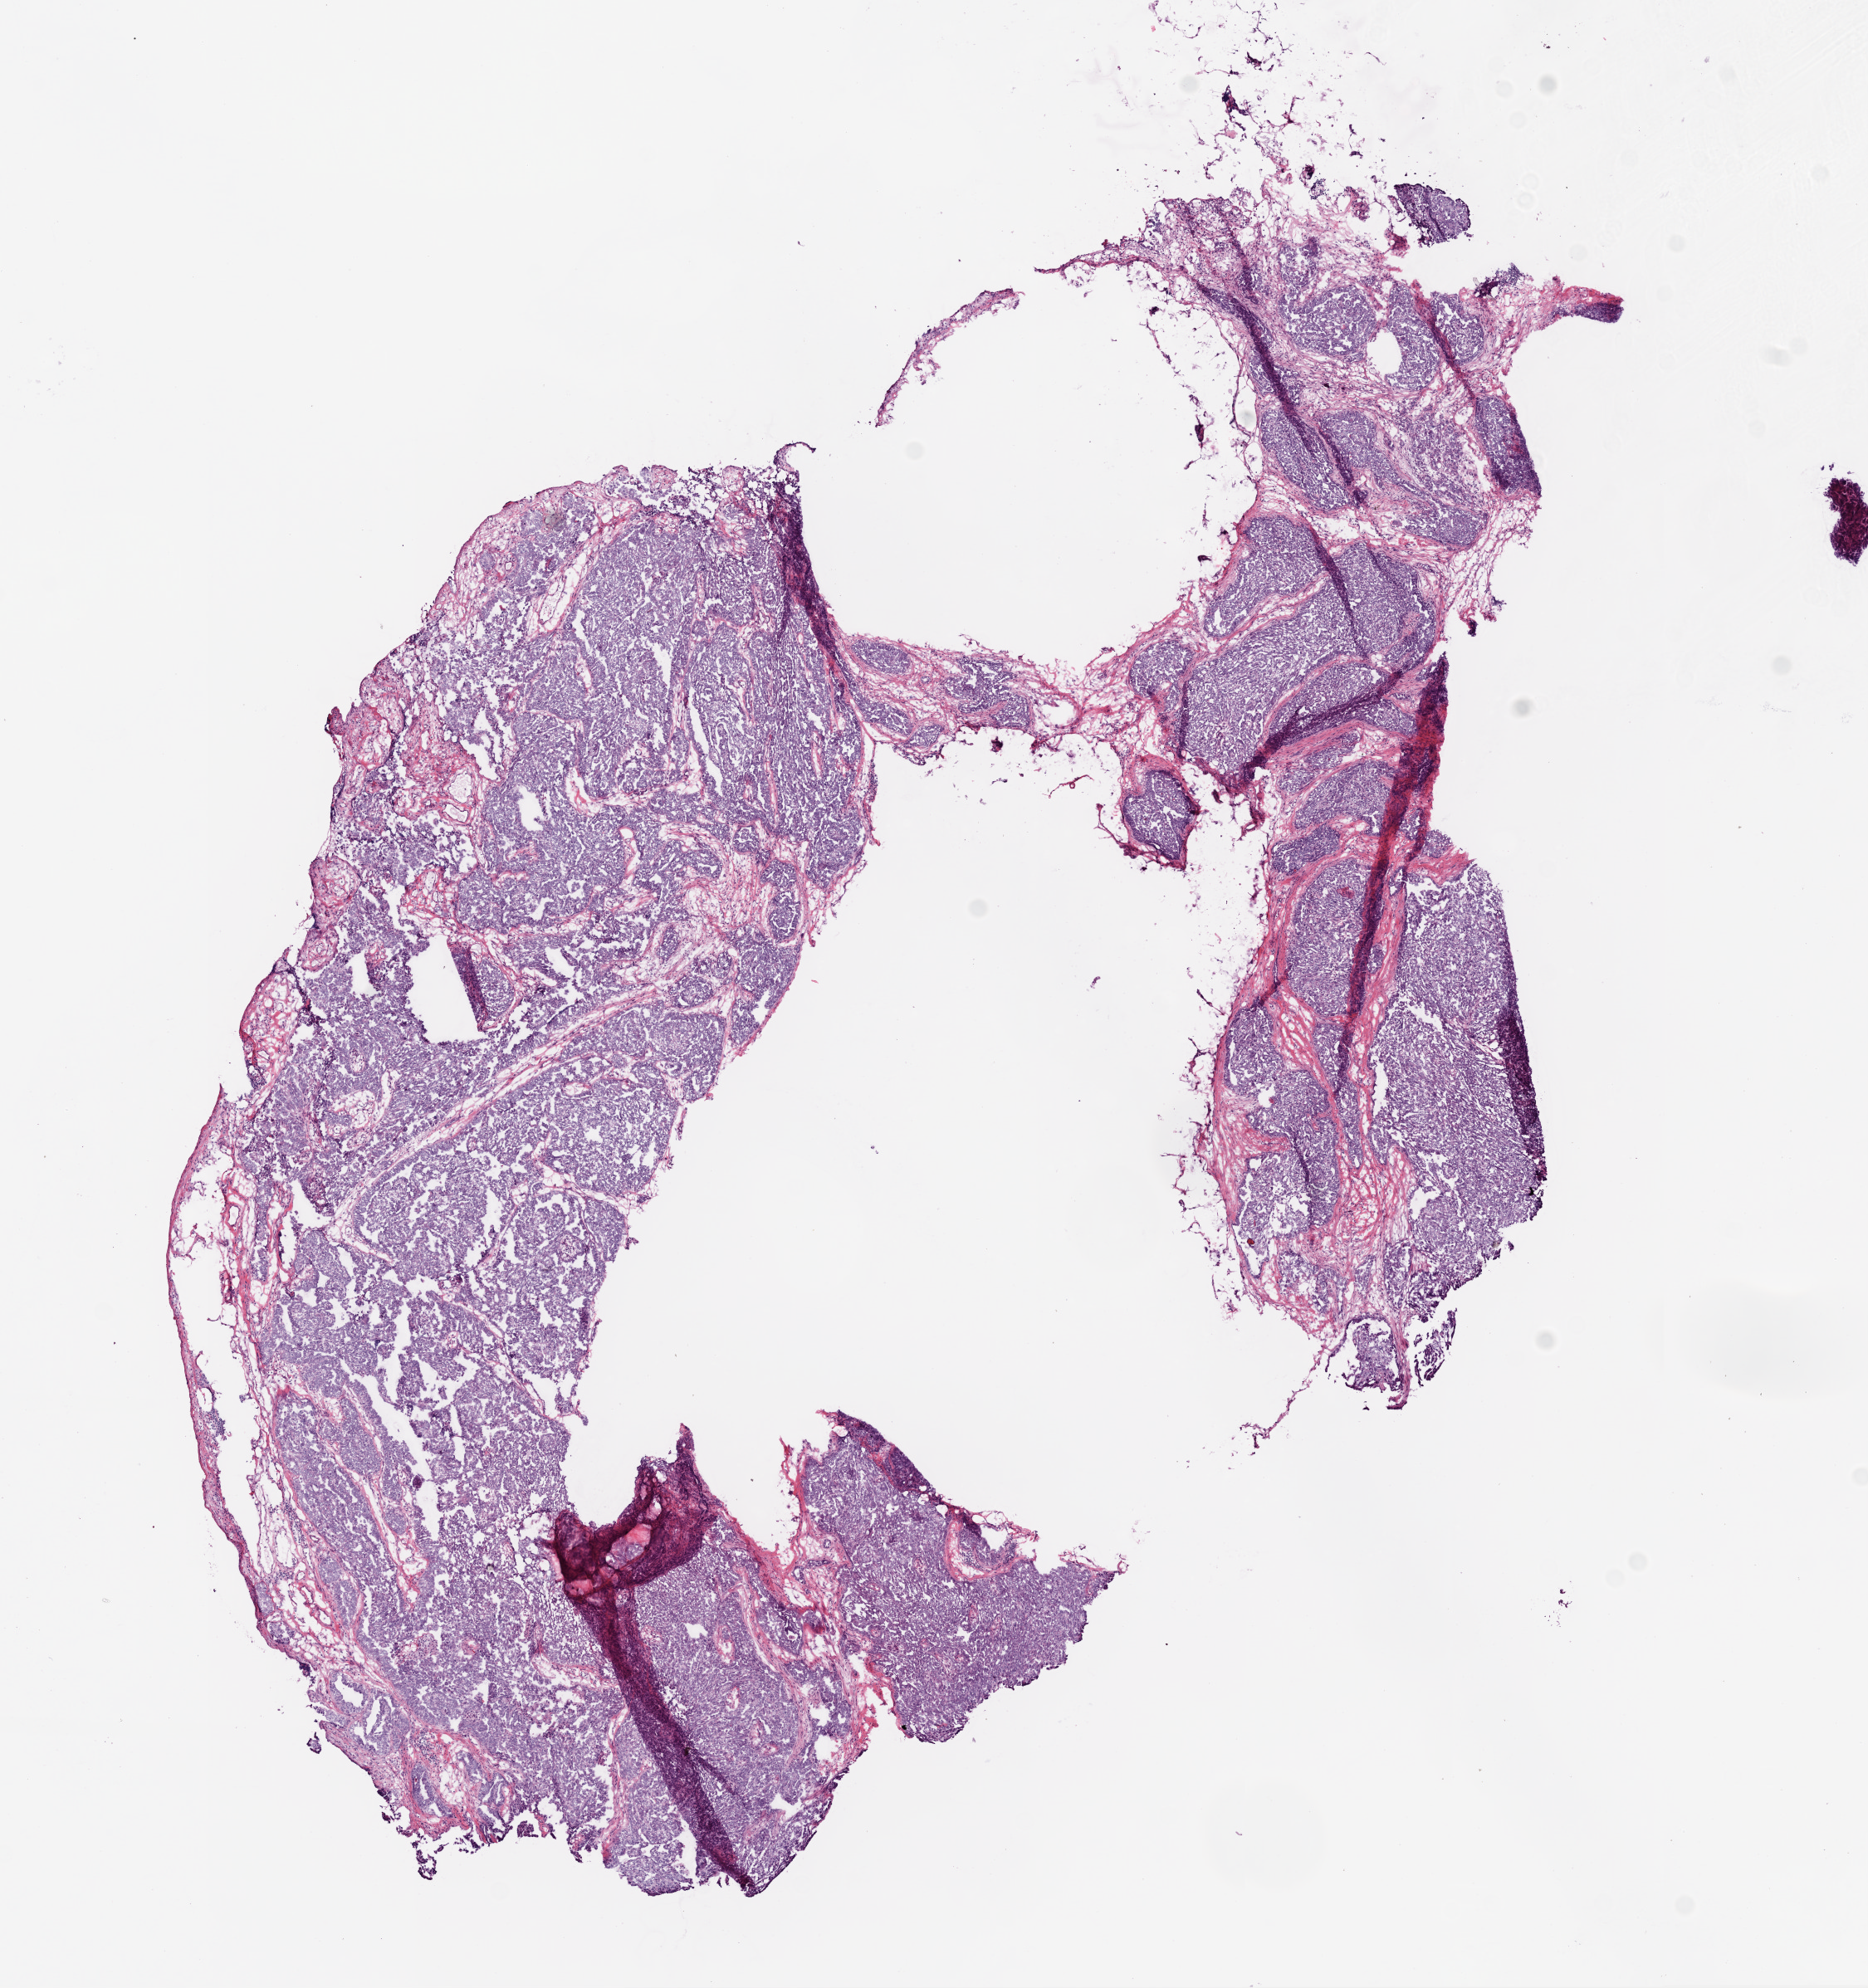
Digitized H&E-stained tissue section (whole slide), shown as a low-resolution overview of the whole scanned area (about 9.0 x 9.6 mm, acquisition: 20x scan); frozen section from the bottom of the tissue portion; sample: primary tumour, ovary. Patient: female, age at initial diagnosis 59 years. Histologic grade: G2 (moderately differentiated). Composition of this section per pathologist review: tumour cells 93%, tumour nuclei 95%, normal cells 0%, stromal cells 7%, necrosis 0%.
* pathologic diagnosis: Serous cystadenocarcinoma, NOS
* FIGO stage: IIIC